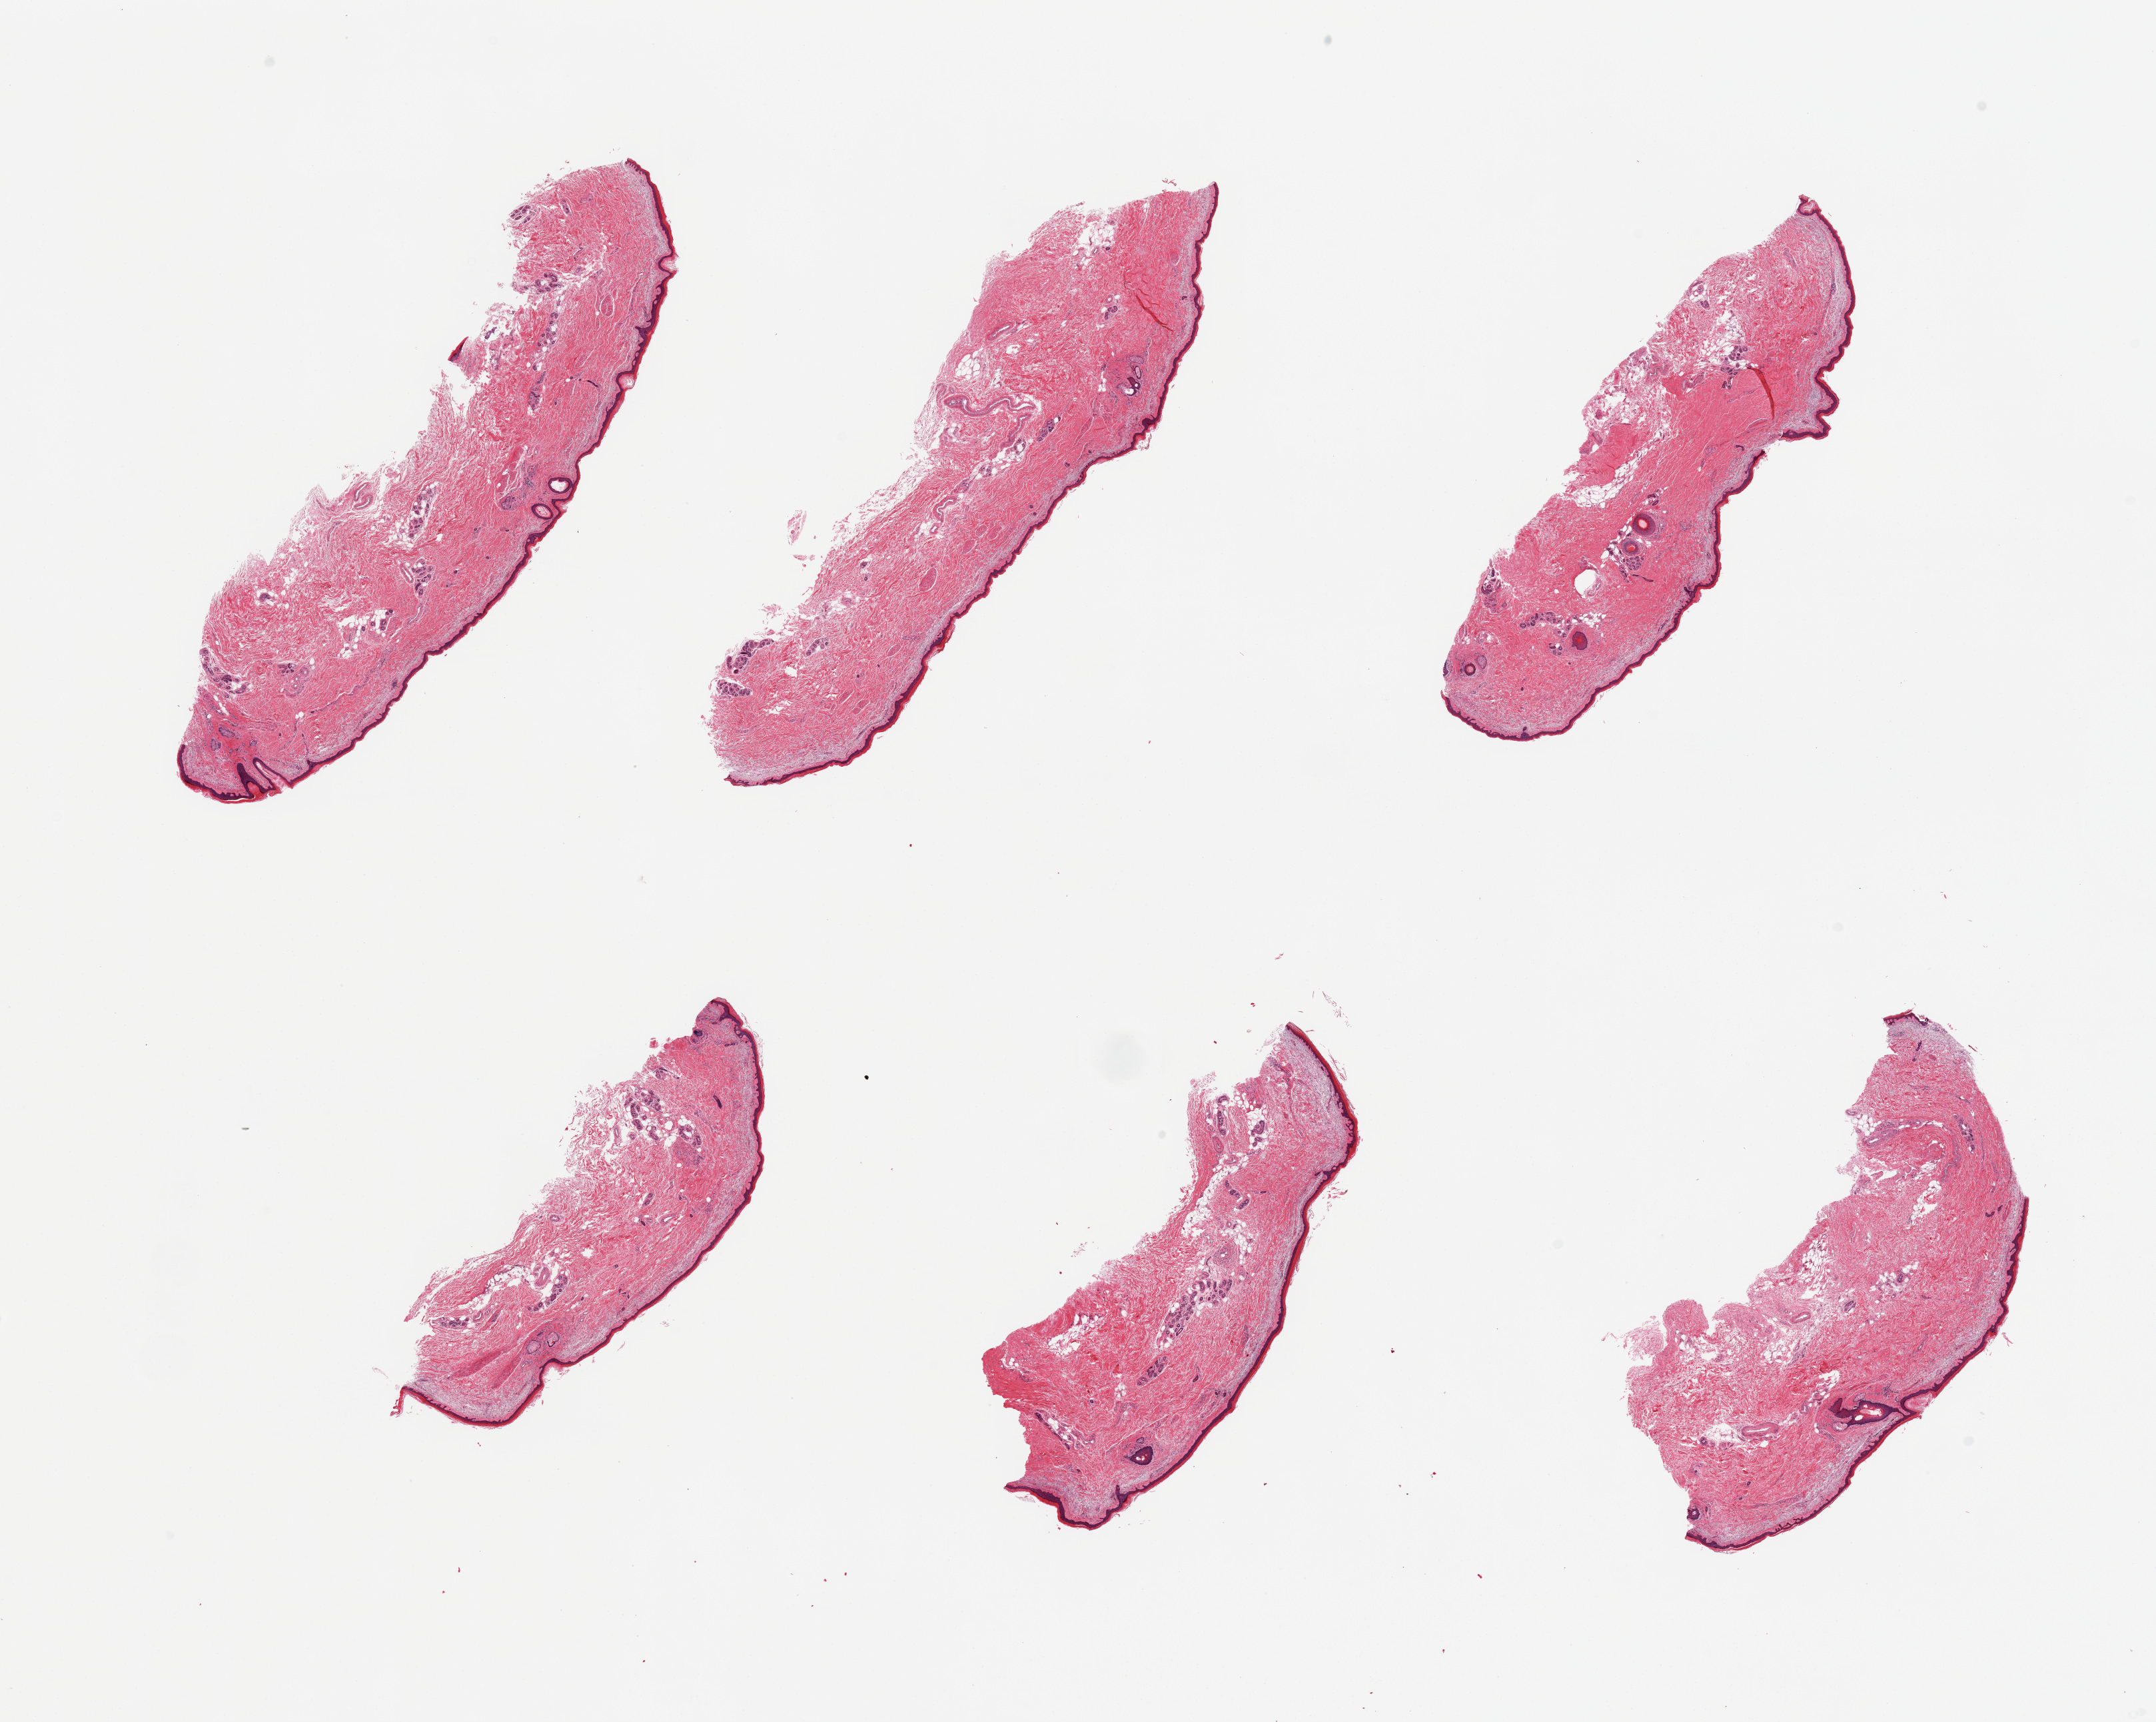
Hematoxylin and eosin (H&E) whole-slide image — low-resolution overview of the scanned area, about 25.6 x 20.4 mm. PAXgene-fixed paraffin-embedded (PFPE) section. Target tissue: skin of lower leg. Tissue donor sample. Donor sex: male.
Reviewer comment on this tissue sample: 6 pieces; 10% to 20% internal fat; solar elastosis.